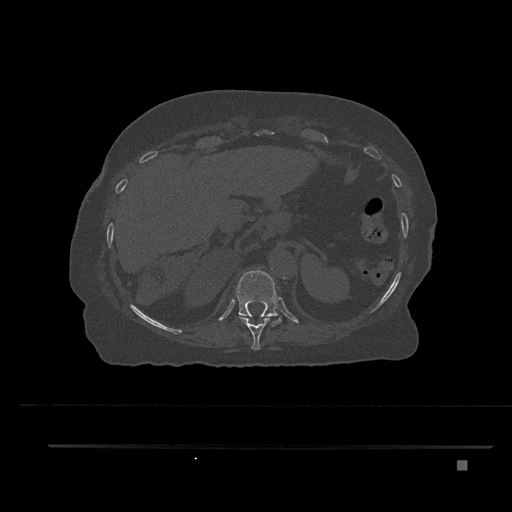
CT including the spine, one axial slice. Position 329 of 797 along the scan axis. Bone window (W 1800 / L 400 HU). 0.5 mm slice thickness. 512 × 512 image matrix. Female patient, age 76 years. From the clinical record (not read from this slice): primary cancer: lung; vertebrae with lytic lesions (as recorded): T11, L3.
Annotated regions visible in this slice (semi-automatically segmented with operator editing):
- T10 vertebra: box from (x=239, y=316) to (x=271, y=350) px
- T11 vertebra: (x=235, y=270)–(x=281, y=326)